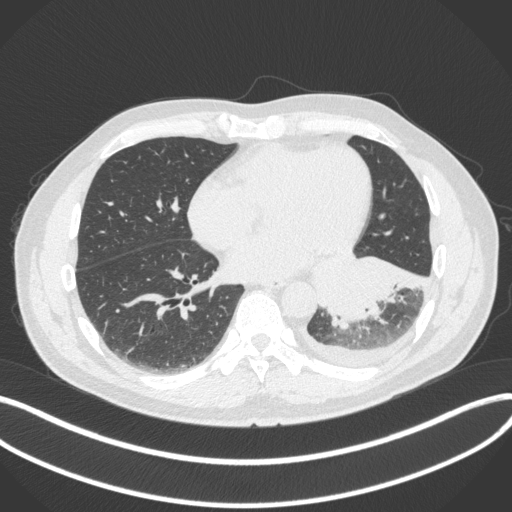
Chest CT, one axial slice; 120 kVp; lung window (W 1500 / L -600 HU); 1 mm slice thickness; 512 × 512 image matrix, field of view 400 × 400 mm. Male patient, age 58 years. From the clinical record (not read from this slice): clinical TNM (as recorded): T3 N1 M1b; histopathological grade: G3.
Outlined on this slice (bounding box drawn by a radiologist):
- lung tumour (recorded histology: small cell carcinoma): bounding box <309,246,433,330> (left, top, right, bottom; pixels)